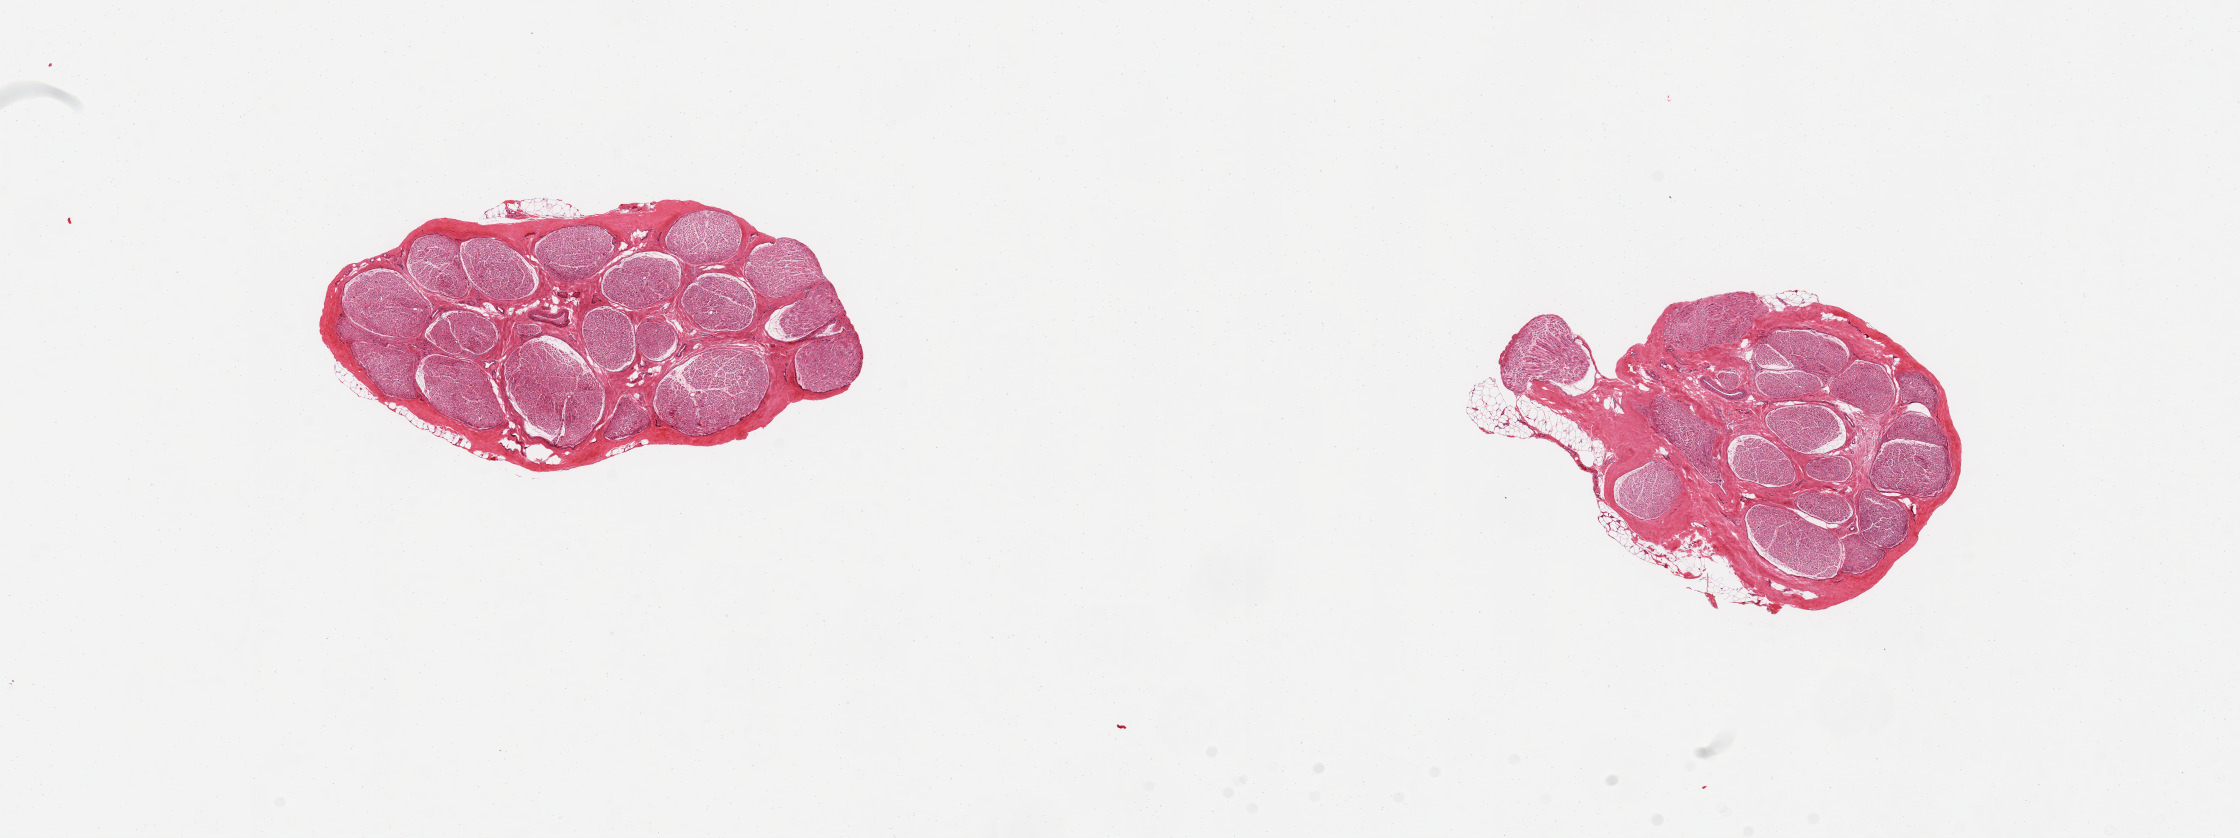
Hematoxylin and eosin (H&E) whole-slide image, a low-resolution overview of the entire scanned area, about 17.7 x 6.6 mm. PAXgene-fixed, paraffin-embedded tissue. Sampled site (target tissue): tibial nerve. Tissue donor sample. Male donor.
Reviewer comment on this tissue sample: 2 pieces; minimal adherent fat.